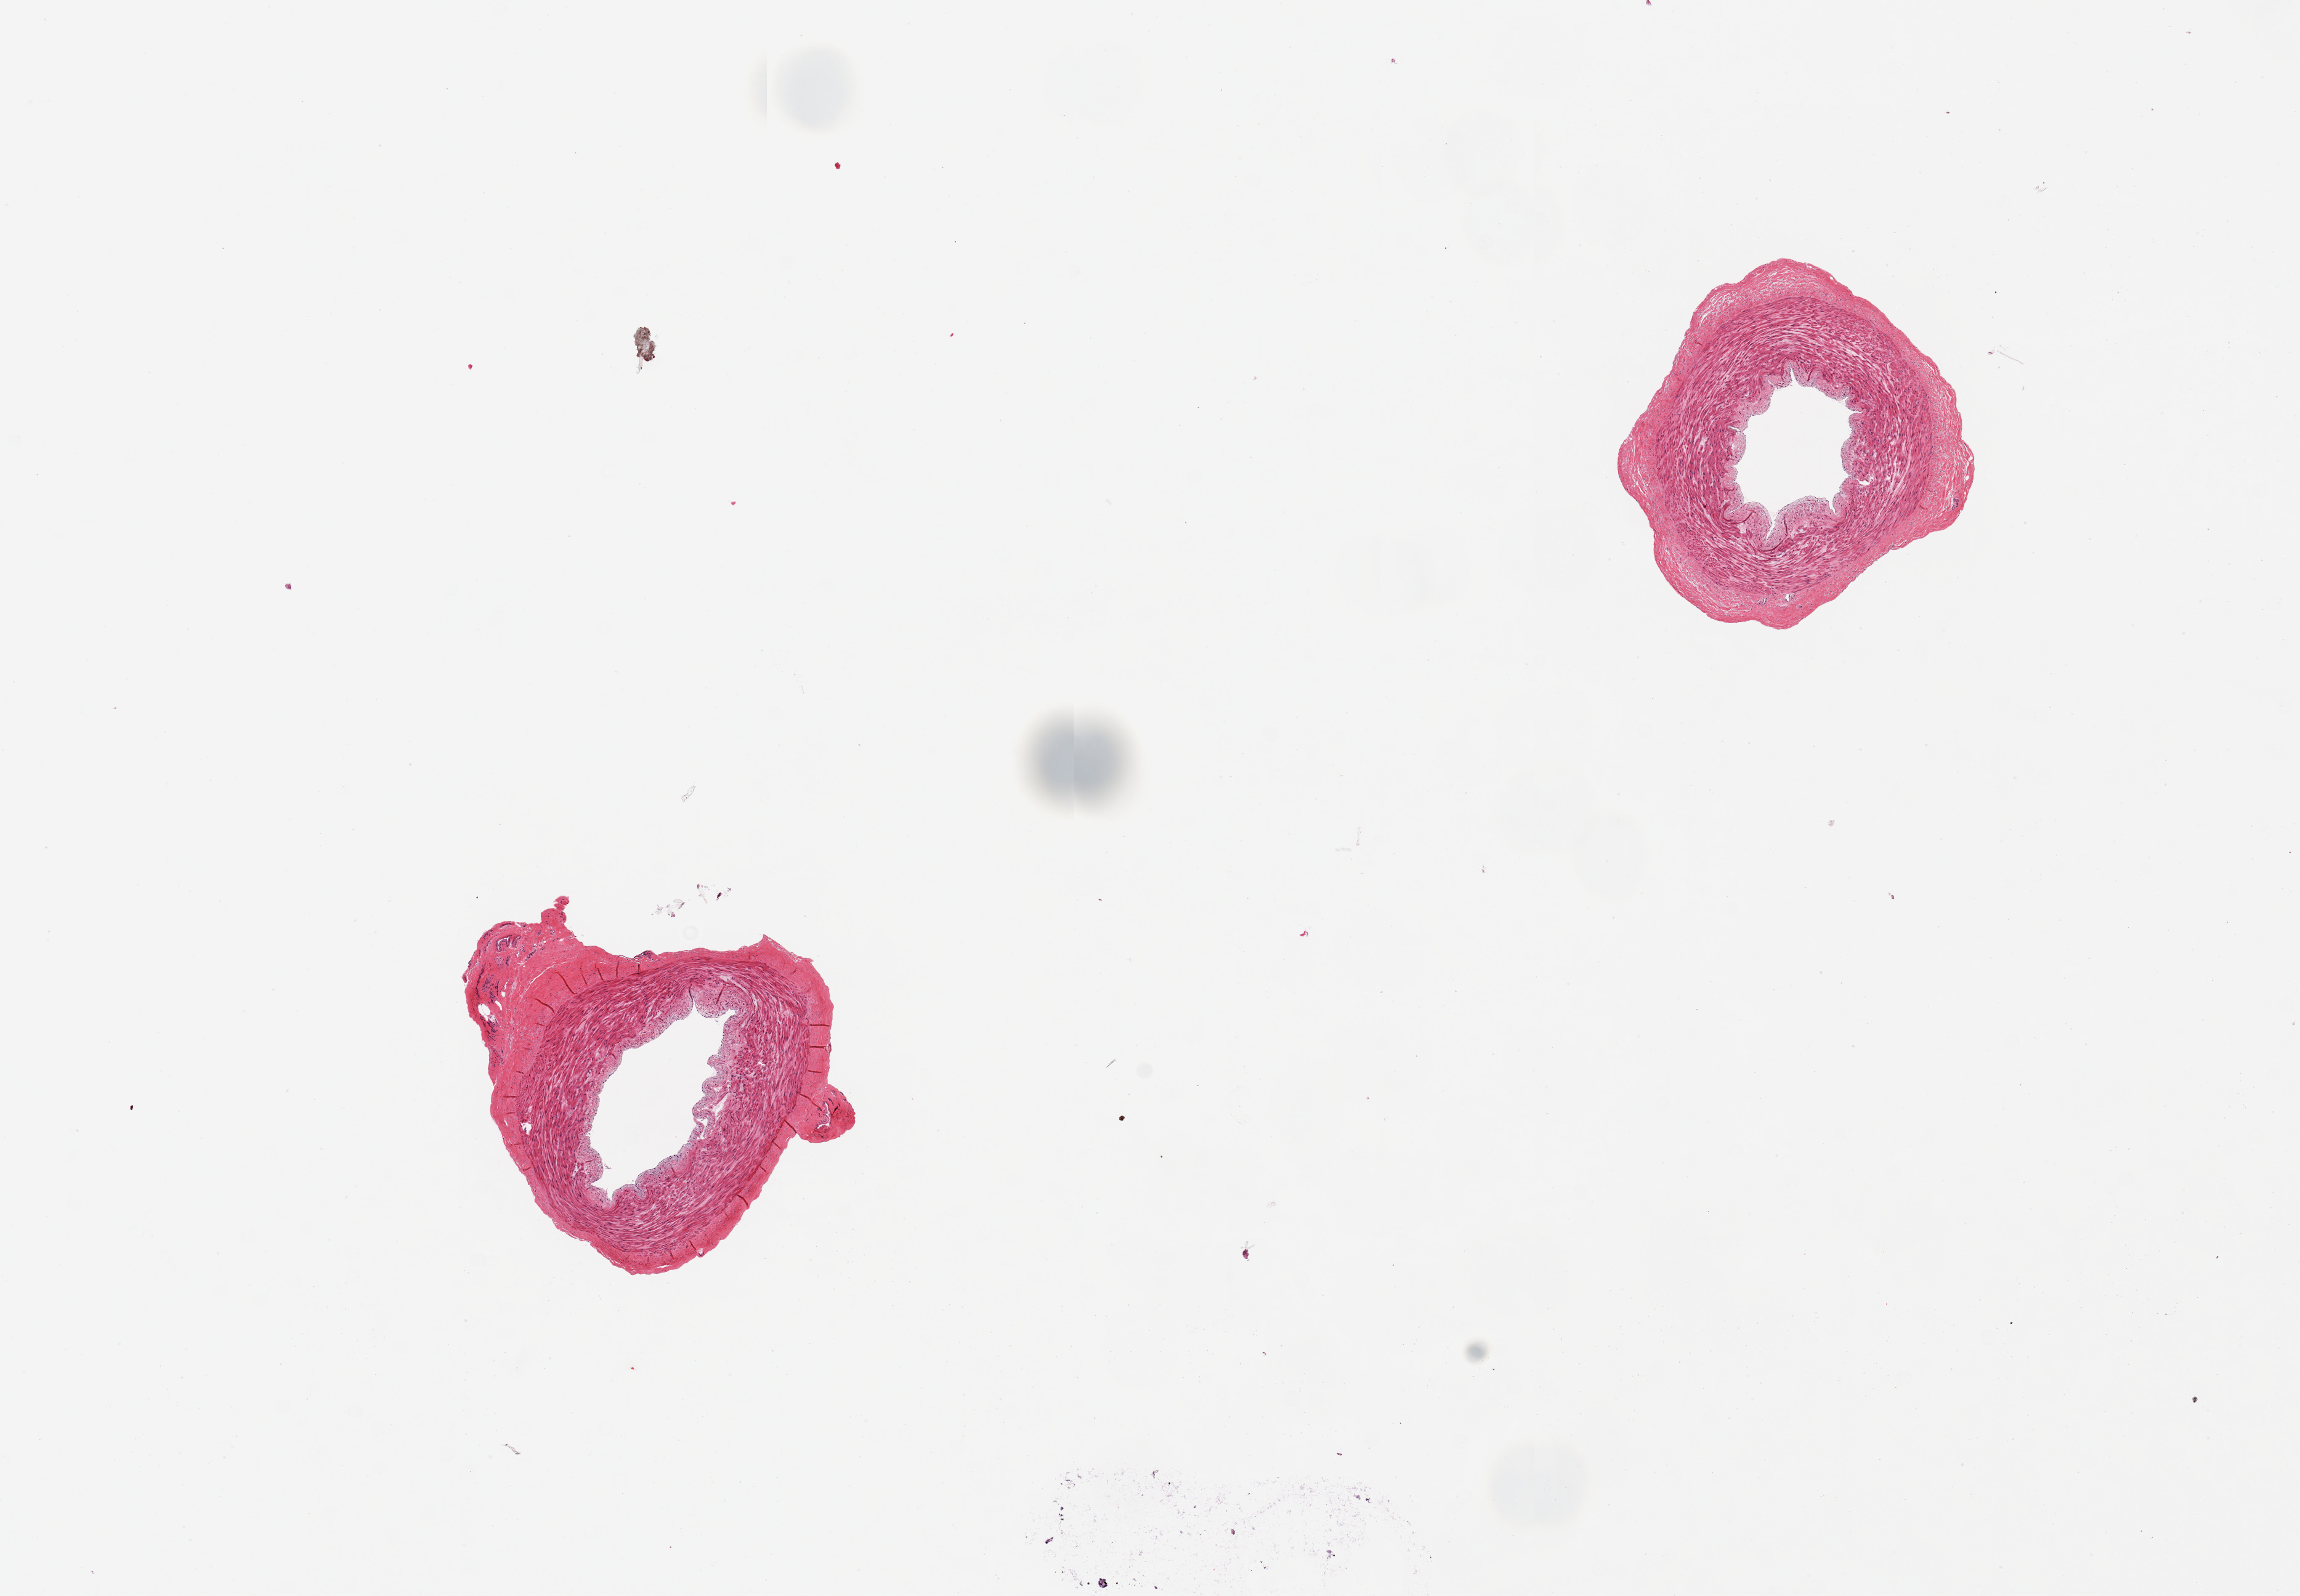
Digitized haematoxylin and eosin-stained section — low-resolution overview of the scanned area, about 14.8 x 10.2 mm (slide scanned at 20x); PAXgene-fixed paraffin-embedded (PFPE) section; target tissue: tibial artery; tissue donor sample.
Reviewer comment on this tissue sample: 2 pieces, good clean specimens, no atherosis noted.